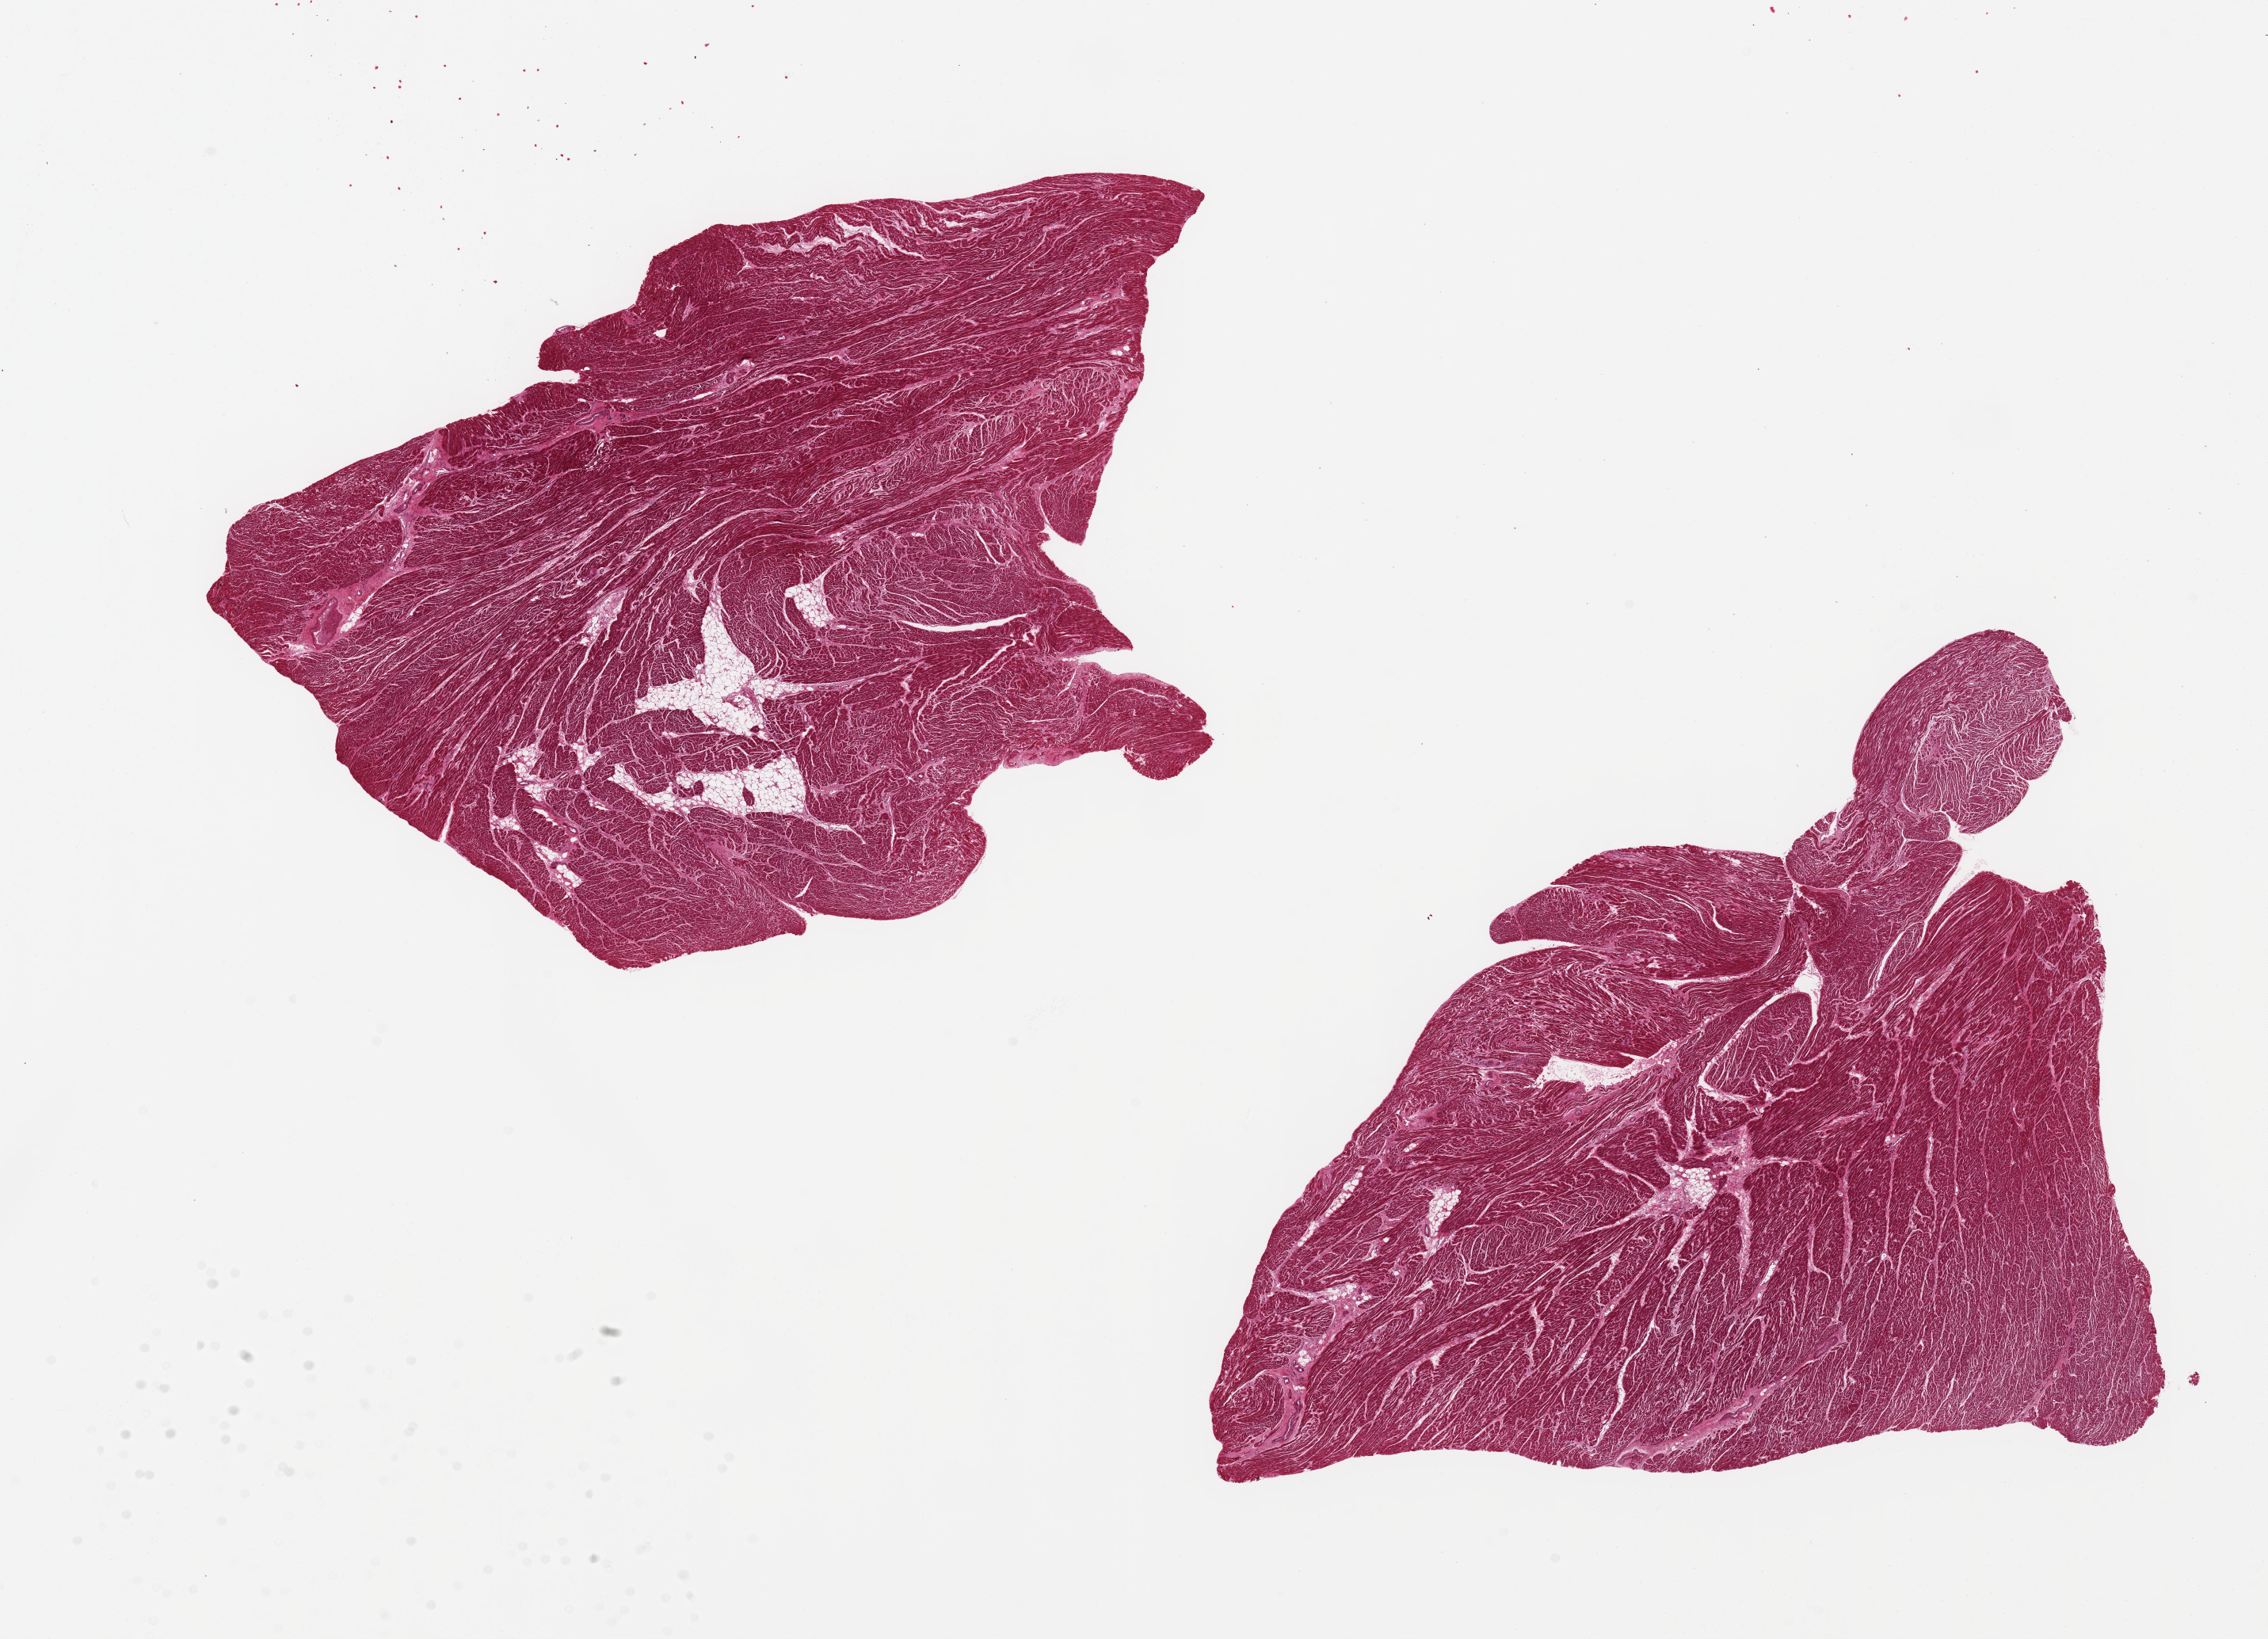
Whole-slide image, haematoxylin and eosin stain, a low-resolution overview of the entire scanned area, about 22.6 x 16.4 mm. PAXgene-fixed, paraffin-embedded tissue. Section of heart (target tissue). Tissue donor sample. Male donor.
- pathologist's review note for this sample: 2 pieces, ~10.5x6 mm; <5% fat; small foci of fibrosis